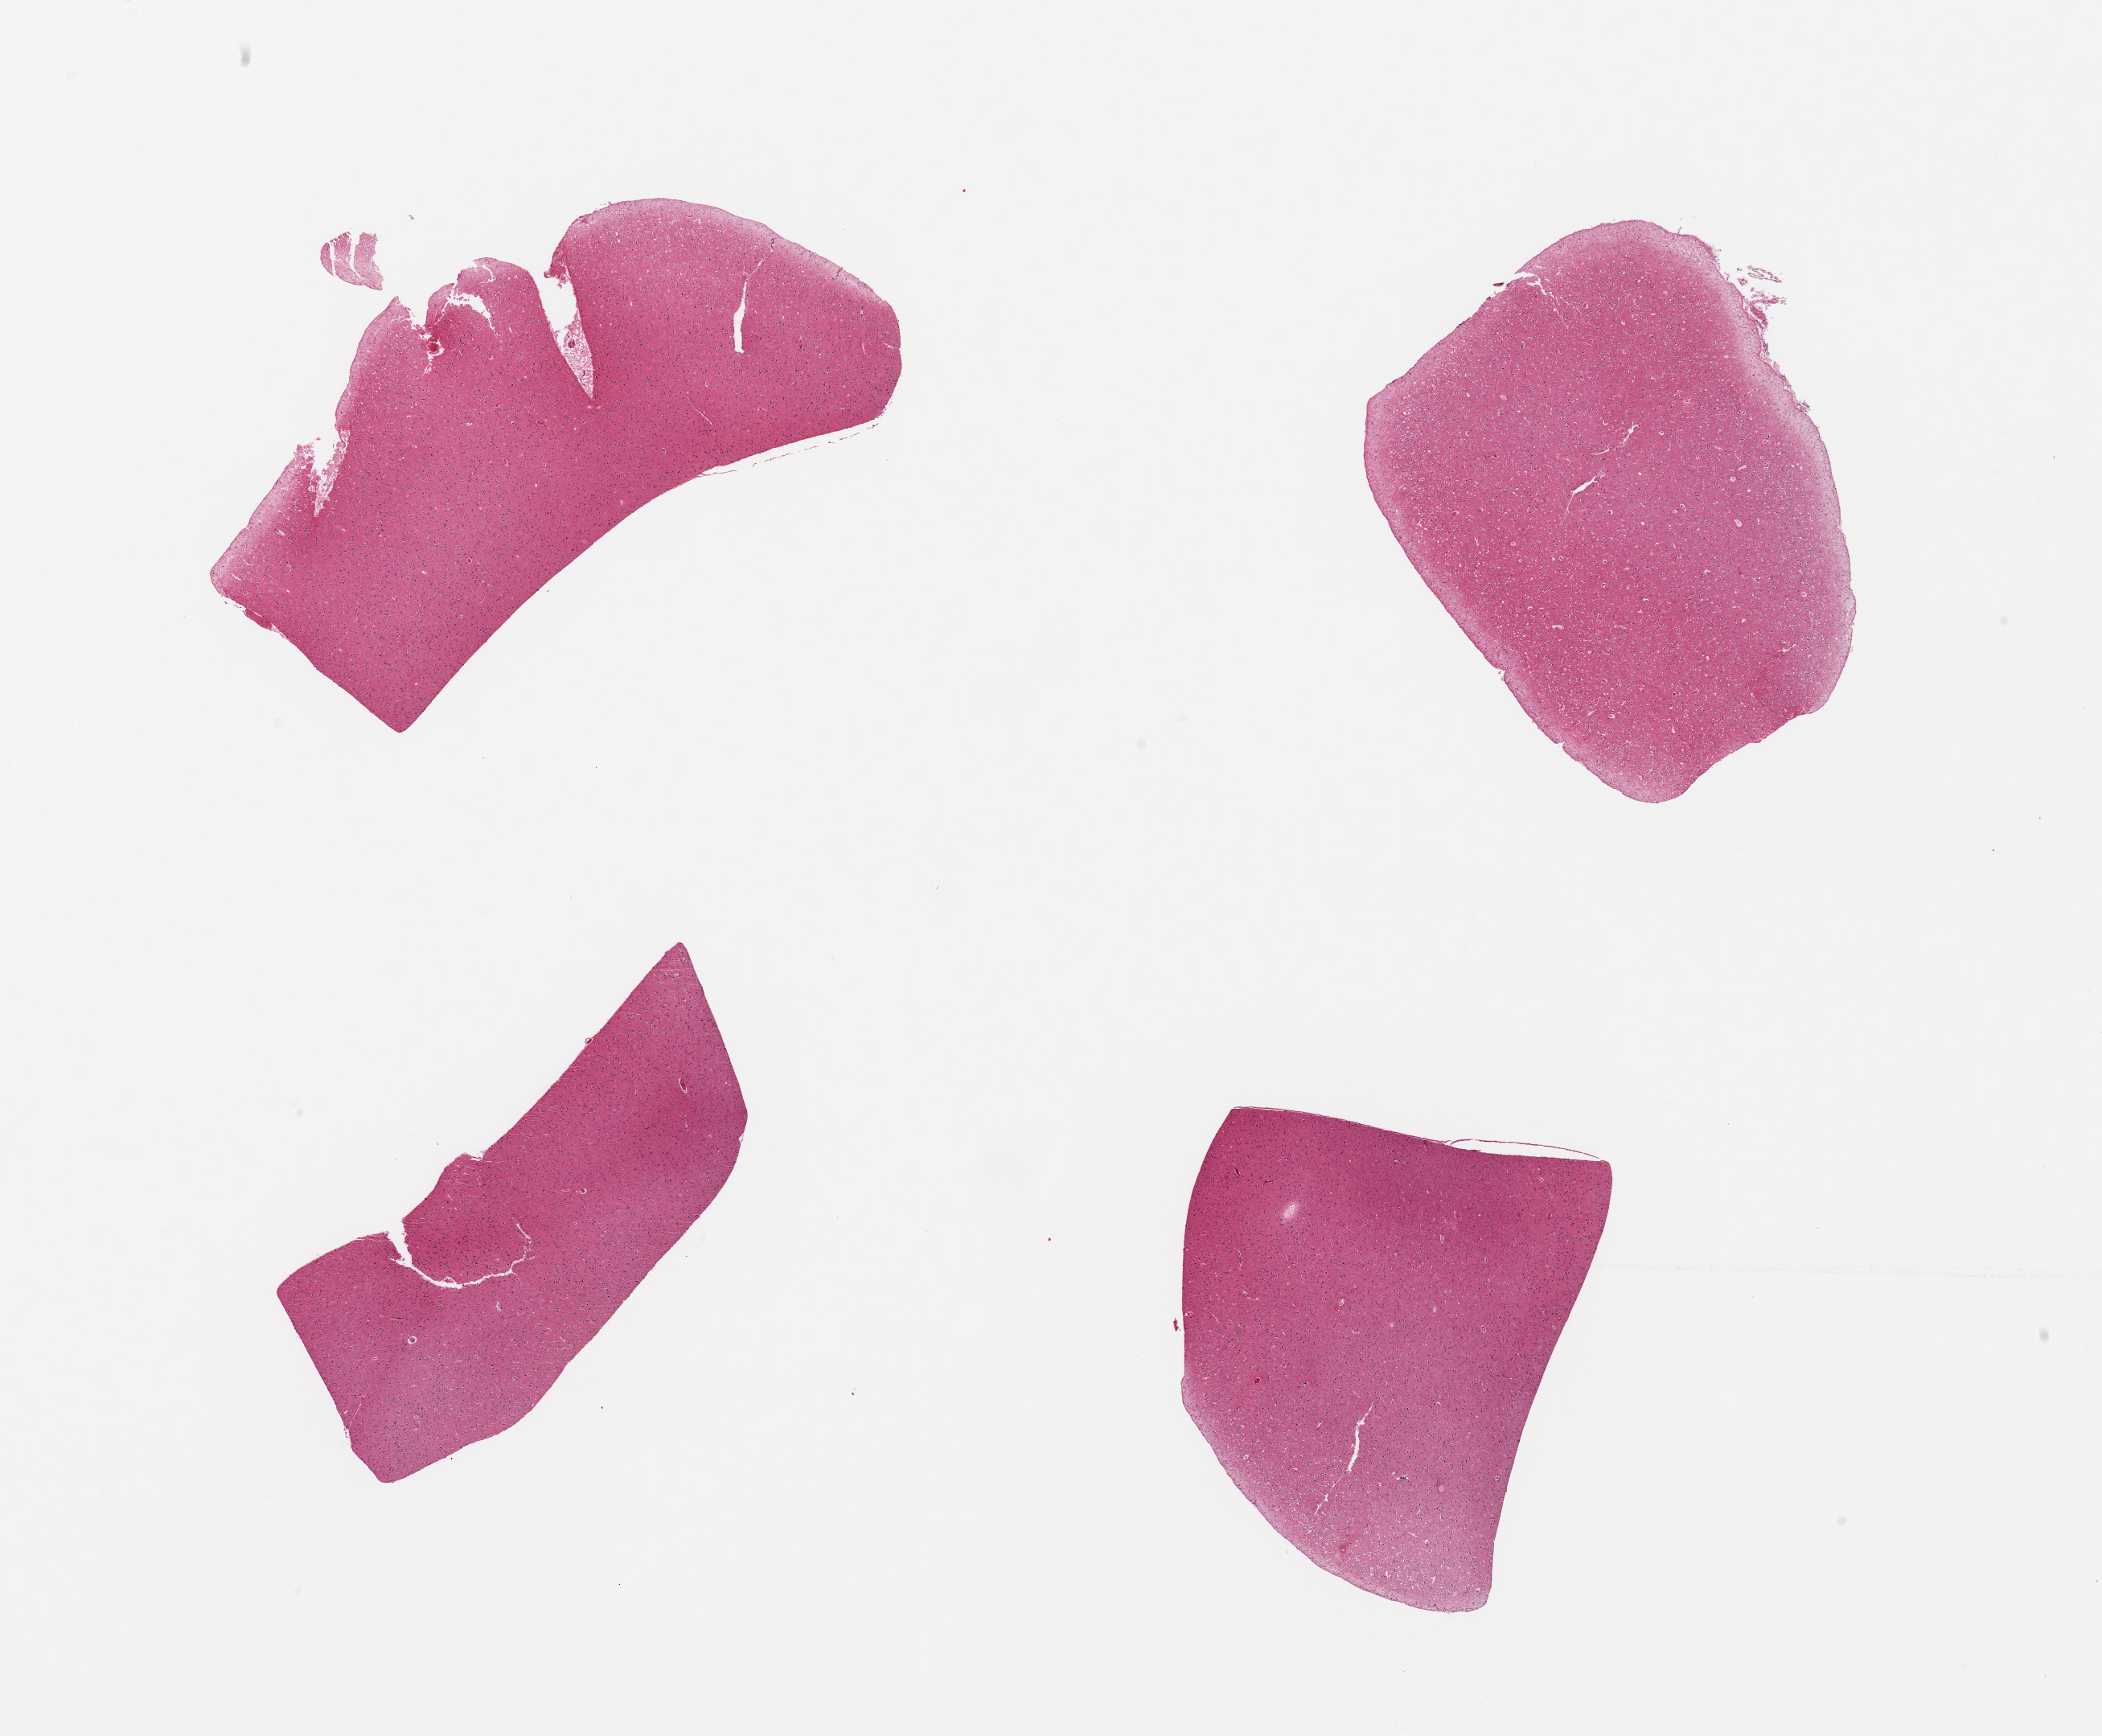
Digitized haematoxylin and eosin-stained section — whole scanned area (about 20.7 x 17.1 mm, from a 20x scan) shown as a low-resolution overview. PAXgene-fixed, paraffin-embedded tissue. Section of cerebral cortex (target tissue). Tissue donor sample. Donor: male.
- review note (as recorded): 2 pieces